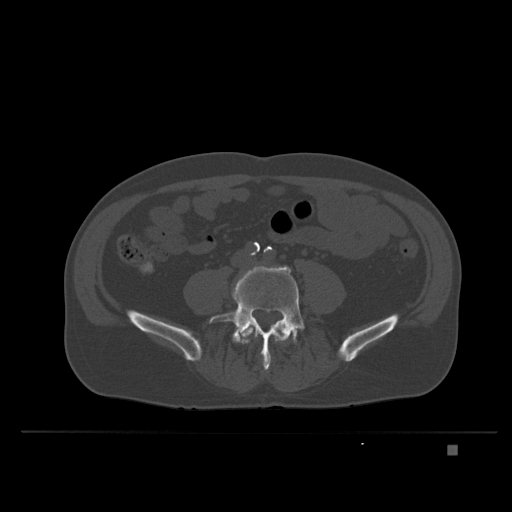
CT including the spine, one axial slice. Position 61 of 435 along the scan axis. Bone window (W 1800 / L 400 HU). 1.5 mm slice thickness. 512 × 512 image matrix, field of view 434 × 434 mm. Patient: male, 73 years. From the clinical record (not read from this slice): primary cancer: skin.
Outlined on this slice (semi-automatically segmented with operator editing):
- L4 vertebra: bounding box [x1, y1, x2, y2] px = [242, 324, 271, 365]
- L5 vertebra: [209, 266, 305, 369]